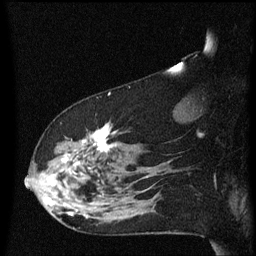
Breast MRI (dynamic contrast-enhanced), one sagittal slice. Slice 42 of 60 in the series (ordered by position). Dynamic contrast-enhanced series, image 2 of 3 at this slice position (ordered by acquisition). 1.5 T. TE 4.2 ms, TR 8.4 ms. 256 × 256 image matrix, field of view 200 × 200 mm. Female patient, age 48 years.
Structures marked on this image (semi-automatically segmented with operator editing):
- analysis volume of interest (the breast-tissue region the enhancement analysis was run in; not a lesion): bounding box (x1, y1, x2, y2) in pixels: (31, 124, 134, 225)
- tumour enhancement mask (voxels above the 70 % enhancement threshold inside the analysis volume of interest): (47, 126, 116, 219)